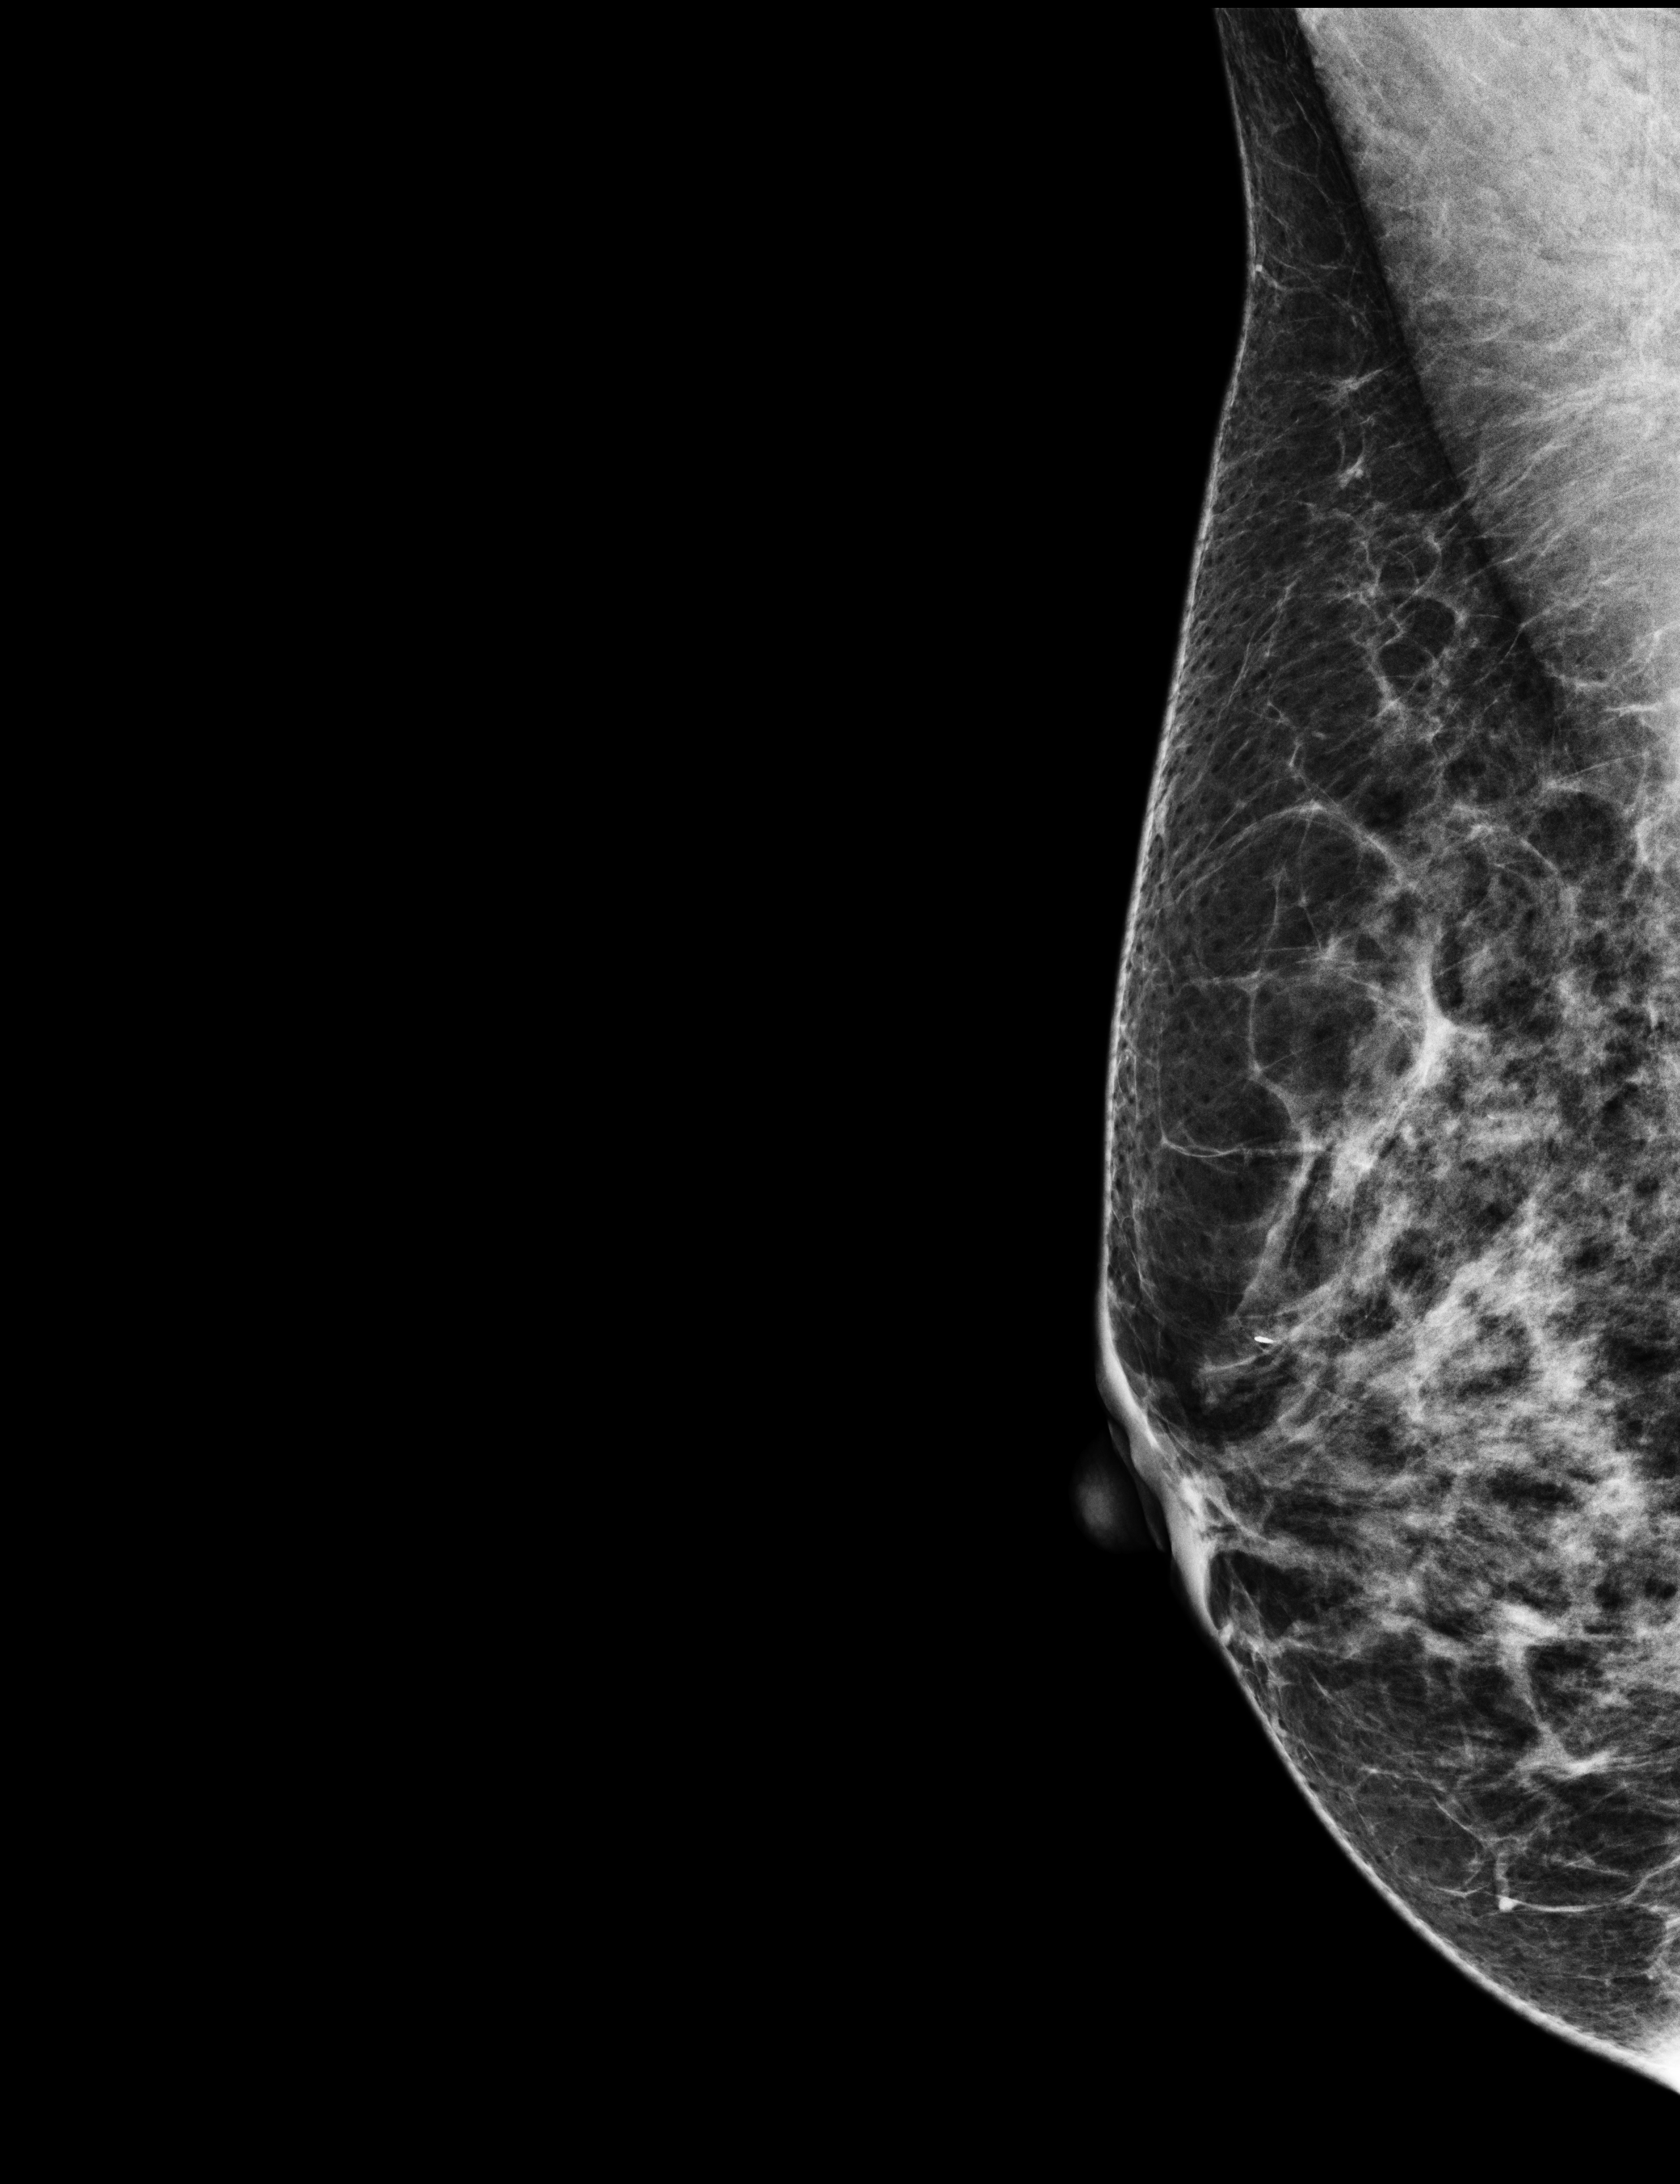
Annual screening mammography examination. Female patient, age 55 years.
Image type: full-field digital mammogram. Breast: right. Projection: MLO view.